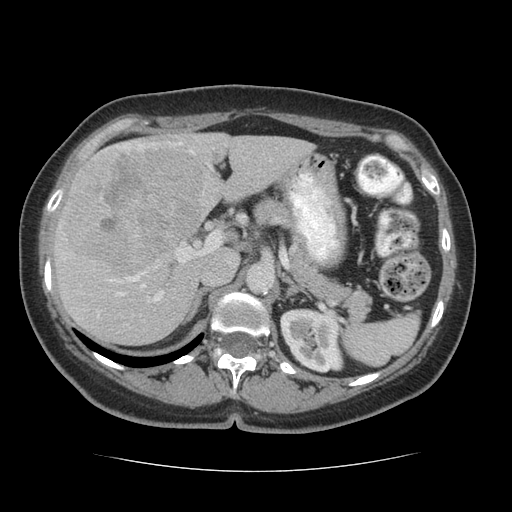
Contrast-enhanced abdominal CT (liver protocol), one axial slice; position 37 of 75 along the scan axis; soft-tissue window (W 400 / L 40 HU); 2.5 mm slice thickness; 512 × 512 image matrix, field of view 360 × 360 mm. From the clinical record (not read from this slice): diagnosis: hepatocellular carcinoma (patient treated with transarterial chemoembolisation; whether this scan precedes or follows treatment is not stated here); TNM stage (as recorded): Stage-I; Child-Pugh class: A; tumour nodularity: uninodular.
Structures marked on this image (semi-automatically segmented with operator editing):
- liver parenchyma outside the tumour (the mass and vessels are separate outlines, so this box may not span the whole liver): bounding box <54,132,313,344> (left, top, right, bottom; pixels)
- mass: <64,146,203,276>
- liver vessels: <59,142,210,317>